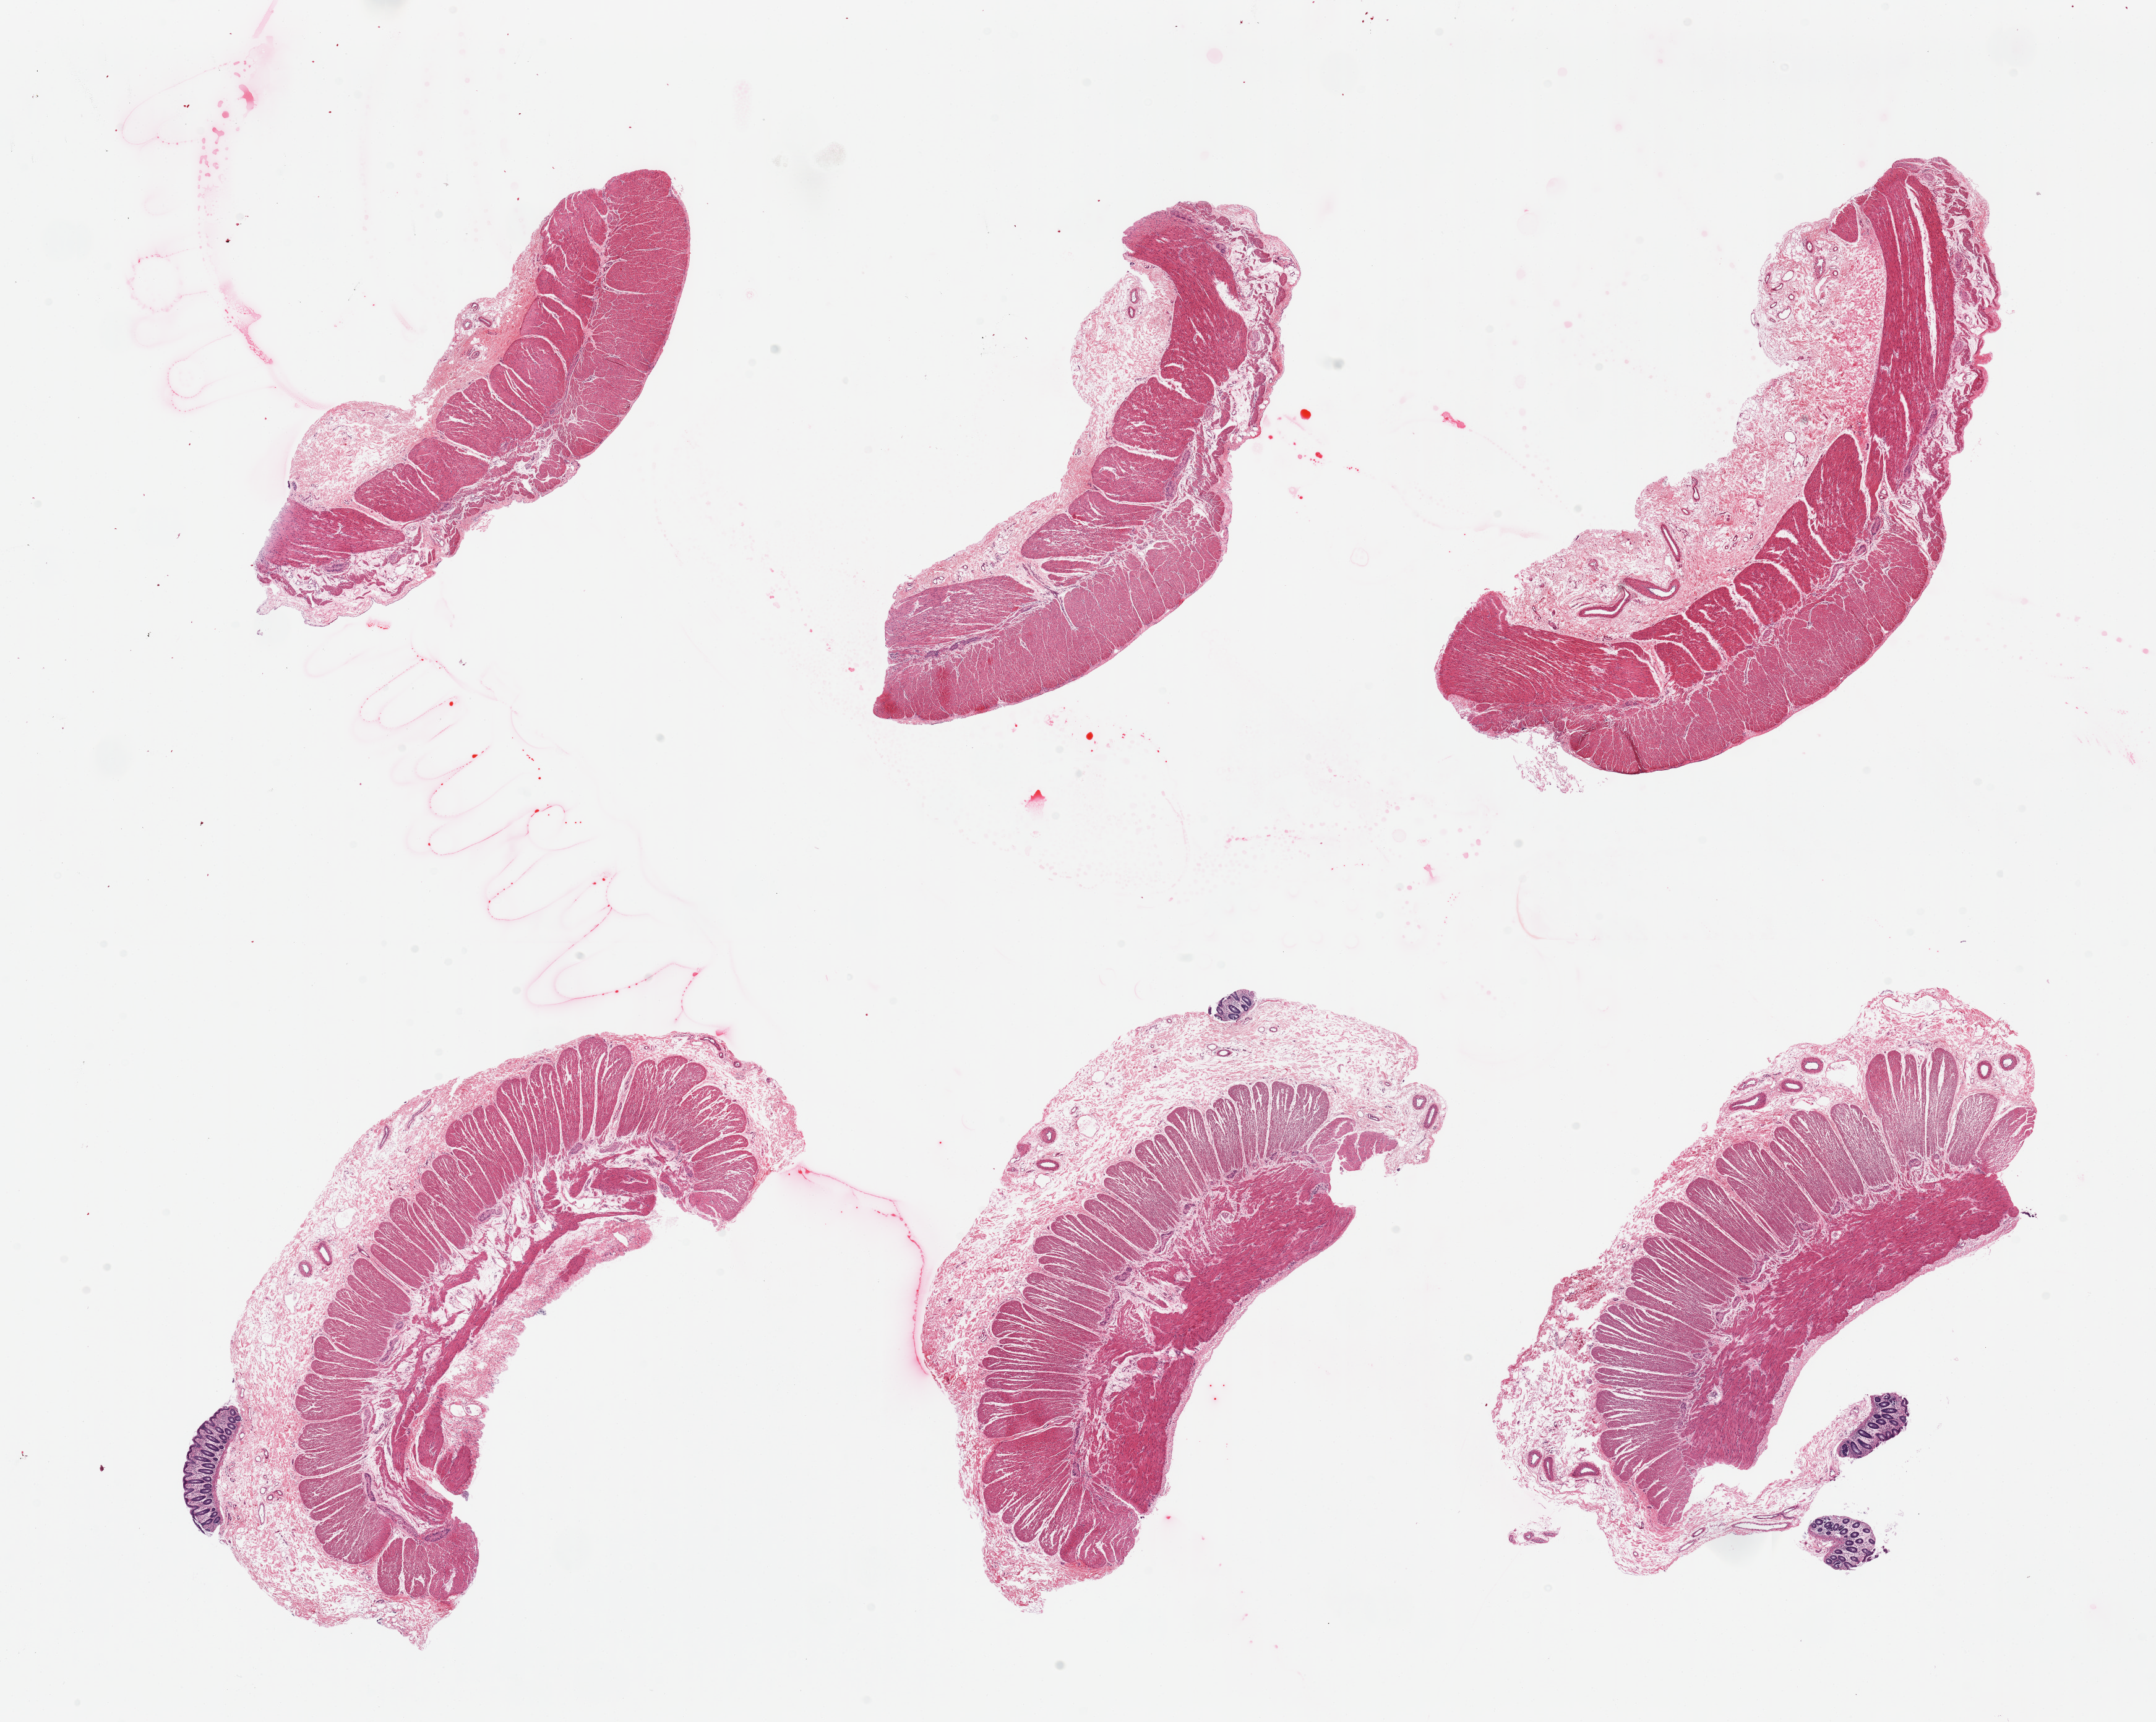
Whole-slide image, hematoxylin and eosin (H&E) stain, brightfield, shown as a low-resolution overview of the whole scanned area (about 27.6 x 22.0 mm, slide scanned at 20x), PAXgene-fixed, paraffin-embedded tissue, sampled site (target tissue): sigmoid colon, donor tissue sample. Donor sex: male.
• pathologist's review note for this sample: 6 pieces, predominantly well trimmed with few strips of mucosa